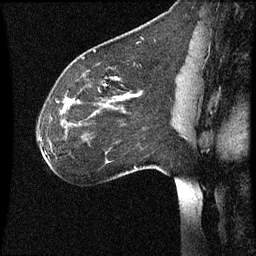
Breast MRI (dynamic contrast-enhanced), one sagittal slice. Position 41 of 60 along the scan axis. Dynamic contrast-enhanced series, image 2 of 3 at this slice position (ordered by acquisition). 1.5 T. TE 4.2 ms, TR 8.9 ms. 2 mm slice thickness. 256 × 256 image matrix. Patient: female, 35 years. Case-level facts recorded for this patient, not image findings: setting: breast cancer imaged before/during neoadjuvant chemotherapy; receptor status: HER2-positive.
Annotated regions visible in this slice (semi-automatic segmentation, software-assisted and operator-edited):
- analysis volume of interest (the breast-tissue region the enhancement analysis was run in; not a lesion): box from (x=35, y=66) to (x=177, y=177) px
- tumour enhancement mask (voxels above the 70 % enhancement threshold inside the analysis volume of interest): (x=129, y=94)–(x=131, y=97)